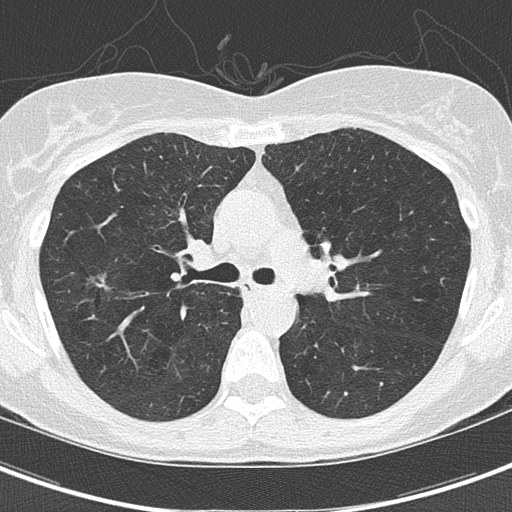
Low-dose screening chest CT, axial slice; third annual screen; lung window (W 1500 / L -600 HU); 2 mm slice thickness; lung (sharp) reconstruction kernel (B50f); slice 55 of 154 in the series; 512 × 512 image matrix. Female, age 59 years at enrolment. Current smoker at enrolment.
Expert reader's lesion annotation, bounding box (x1, y1, x2, y2) in pixels: (69, 261, 128, 314). Reader record for this screening exam (exam-level; its link to the box is not recorded): non-calcified nodule or mass ≥4 mm, right upper lobe, 10 × 8 mm, poorly defined margins, ground glass attenuation, pre-existing on the prior screen: yes; interval growth: yes. Later outcome: lung cancer diagnosed 63 days after this screen — bronchiolo-alveolar adenocarcinoma, NOS, right upper lobe, well differentiated (G1), stage IA (AJCC 6th edition), 4 mm at pathology.